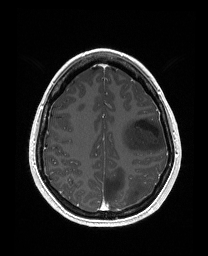
Brain MRI from a brain-tumour surgery series, one axial slice. Slice 116 of 176 in the series (ordered by position). T1-weighted post-contrast. 1 mm slice thickness. 208 × 256 image matrix, field of view 203 × 250 mm. Case-level facts recorded for this patient, not image findings: histopathology: Astrocytoma; WHO grade: 3; IDH mutation: yes; tumour location: Left Frontal.
Annotated regions visible in this slice (manually delineated by an expert):
- tumour: box from (x=121, y=117) to (x=166, y=153) px